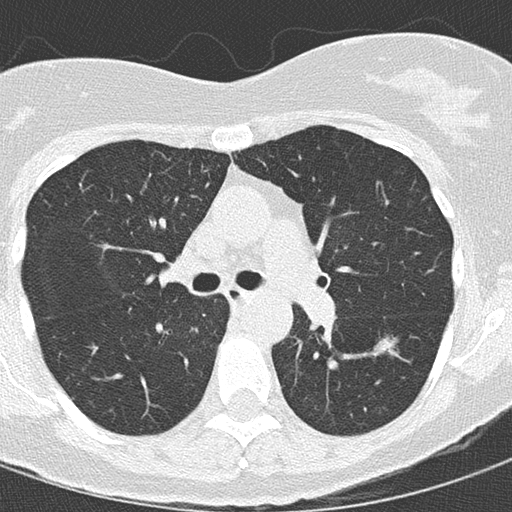
Chest CT (low-dose screening protocol), one axial image; first (baseline) screen; lung window (W 1500 / L -600 HU); 2 mm slice thickness; 120 kVp; slice 55 of 145 in the series; 512 × 512 image matrix, field of view 270 × 270 mm. Female, age 68 years at enrolment. Current smoker at enrolment.
Expert reader's lesion annotation, bounding box [x1, y1, x2, y2] px = [369, 323, 414, 366]. Reader record for this screening exam (exam-level; its link to the box is not recorded): non-calcified nodule or mass ≥4 mm, left lower lobe, 15 × 15 mm, mixed attenuation. Official screen result: positive, change unspecified: nodule(s) >= 4 mm or enlarging nodule(s), mass(es), or other non-specific abnormalities suspicious for lung cancer.